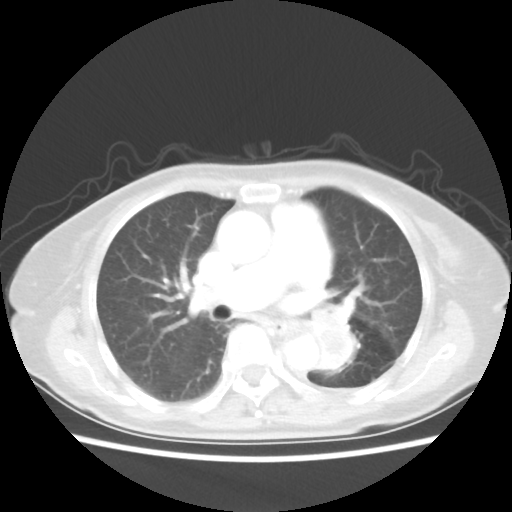
Chest CT, one axial slice. Slice 28 of 50 in the series (ordered by position). Reconstruction kernel STANDARD. 80 kVp. Lung window (W 1500 / L -600 HU). 512 × 512 image matrix, field of view 335 × 335 mm. Female patient, age 81 years. From the clinical record (not read from this slice): clinical TNM (as recorded): T2 N0 M1a.
Structures marked on this image (bounding box drawn by a radiologist):
- lung tumour (recorded histology: squamous cell carcinoma): bounding box <303,312,359,374> (left, top, right, bottom; pixels)